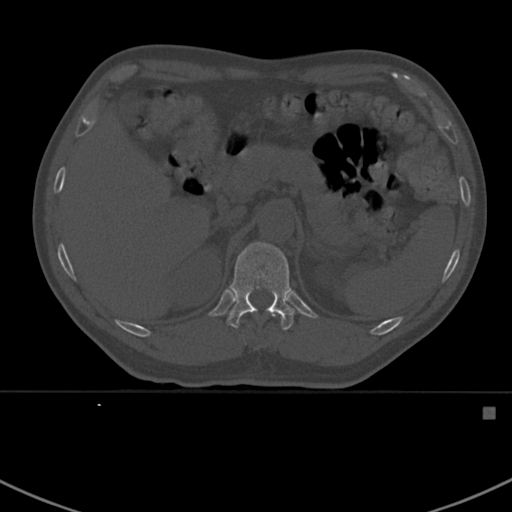
CT including the spine, one axial slice; slice 333 of 412 in the series (ordered by position); reconstruction kernel Br40s; bone window (W 1800 / L 400 HU); 512 × 512 image matrix, field of view 358 × 358 mm. Patient: male, 59 years. Case-level facts recorded for this patient, not image findings: primary cancer: prostate.
Structures marked on this image (semi-automatic segmentation, software-assisted and operator-edited):
- T11 vertebra: bounding box <272,315,275,318> (left, top, right, bottom; pixels)
- T12 vertebra: <226,241,295,330>